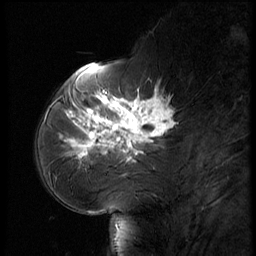
Breast MRI (dynamic contrast-enhanced), one sagittal slice; slice 21 of 56 in the series (ordered by position); dynamic contrast-enhanced series, image 2 of 3 at this slice position (ordered by acquisition); 1.5 T; TE 4.2 ms, TR 9 ms; 2.5 mm slice thickness; 256 × 256 image matrix. Female patient, age 61 years. From the clinical record (not read from this slice): setting: breast cancer imaged before/during neoadjuvant chemotherapy; receptor status: HR-positive, HER2-negative.
Outlined on this slice (semi-automatically segmented with operator editing):
- analysis volume of interest (the breast-tissue region the enhancement analysis was run in; not a lesion): bounding box <65,74,185,175> (left, top, right, bottom; pixels)
- tumour enhancement mask (voxels above the 140 % enhancement threshold inside the analysis volume of interest): <67,85,175,161>